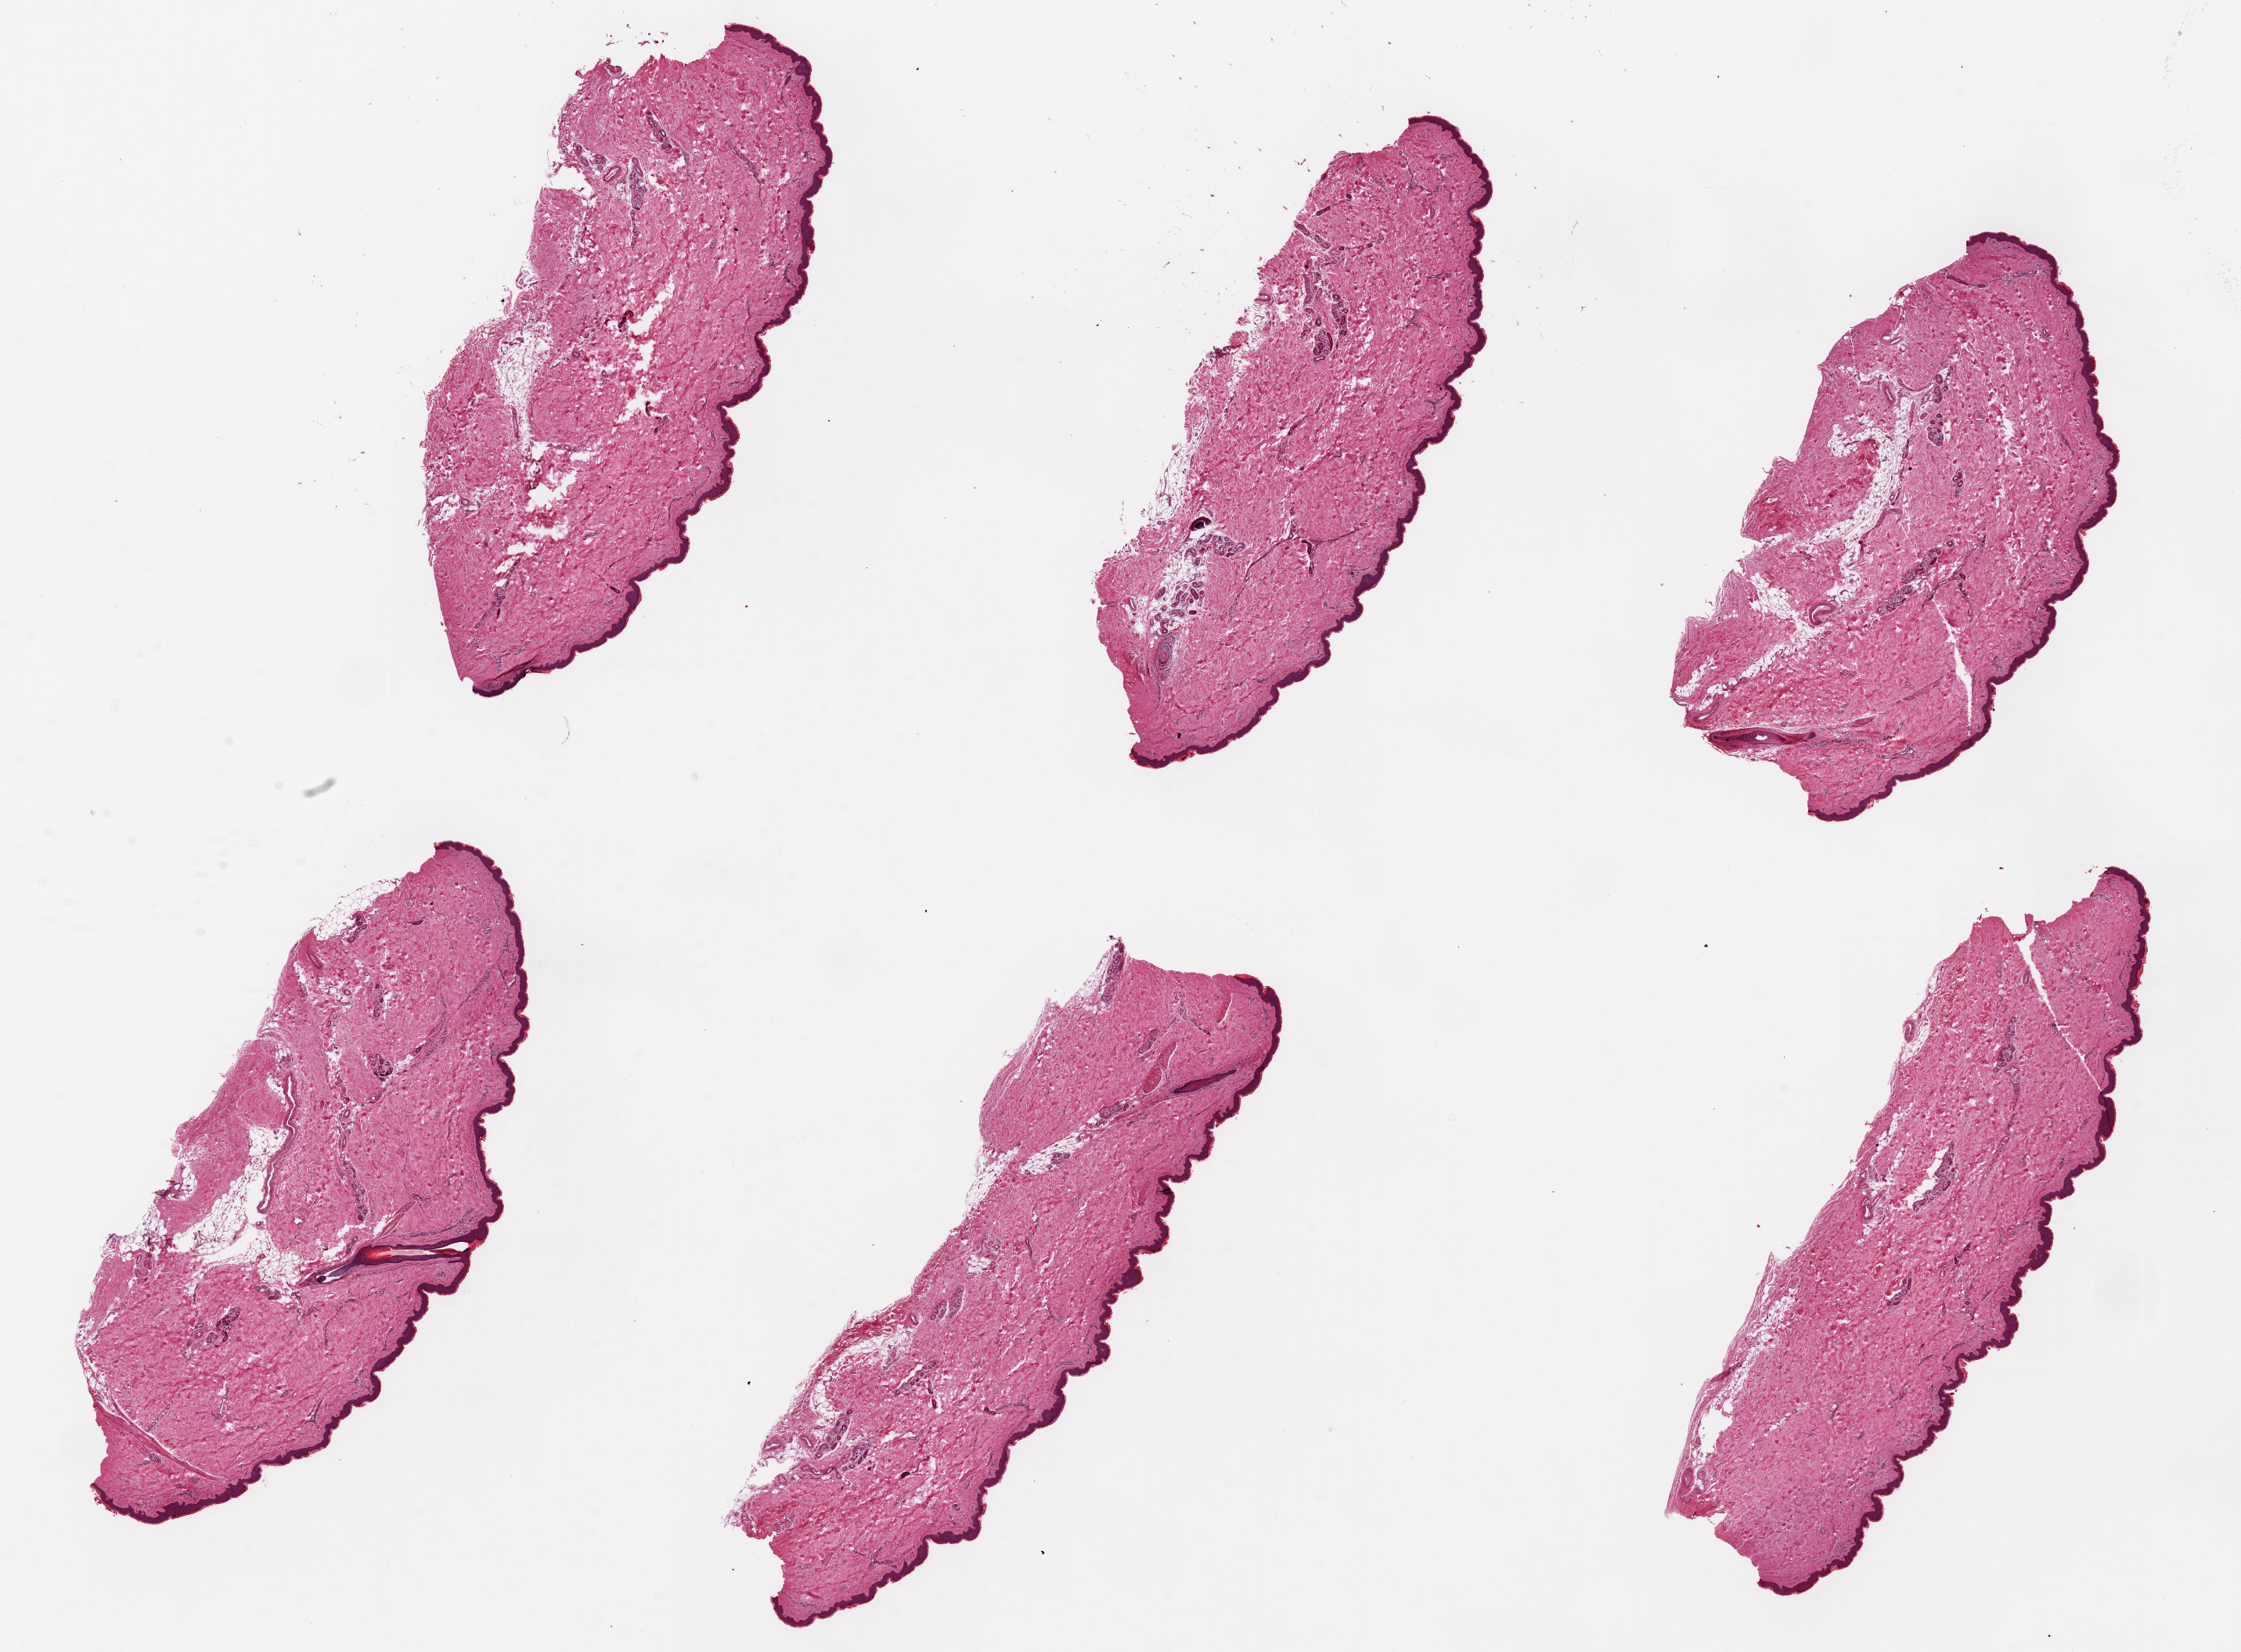
H&E whole-slide image, shown as a low-resolution overview of the whole scanned area (about 22.6 x 16.7 mm); PAXgene-fixed paraffin-embedded (PFPE) section; section of skin of lower leg (target tissue); tissue donor sample. Donor sex: male.
Reviewer comment on this tissue sample: 6 pieces up to 8x3 mm; no subcutaneous adipose.